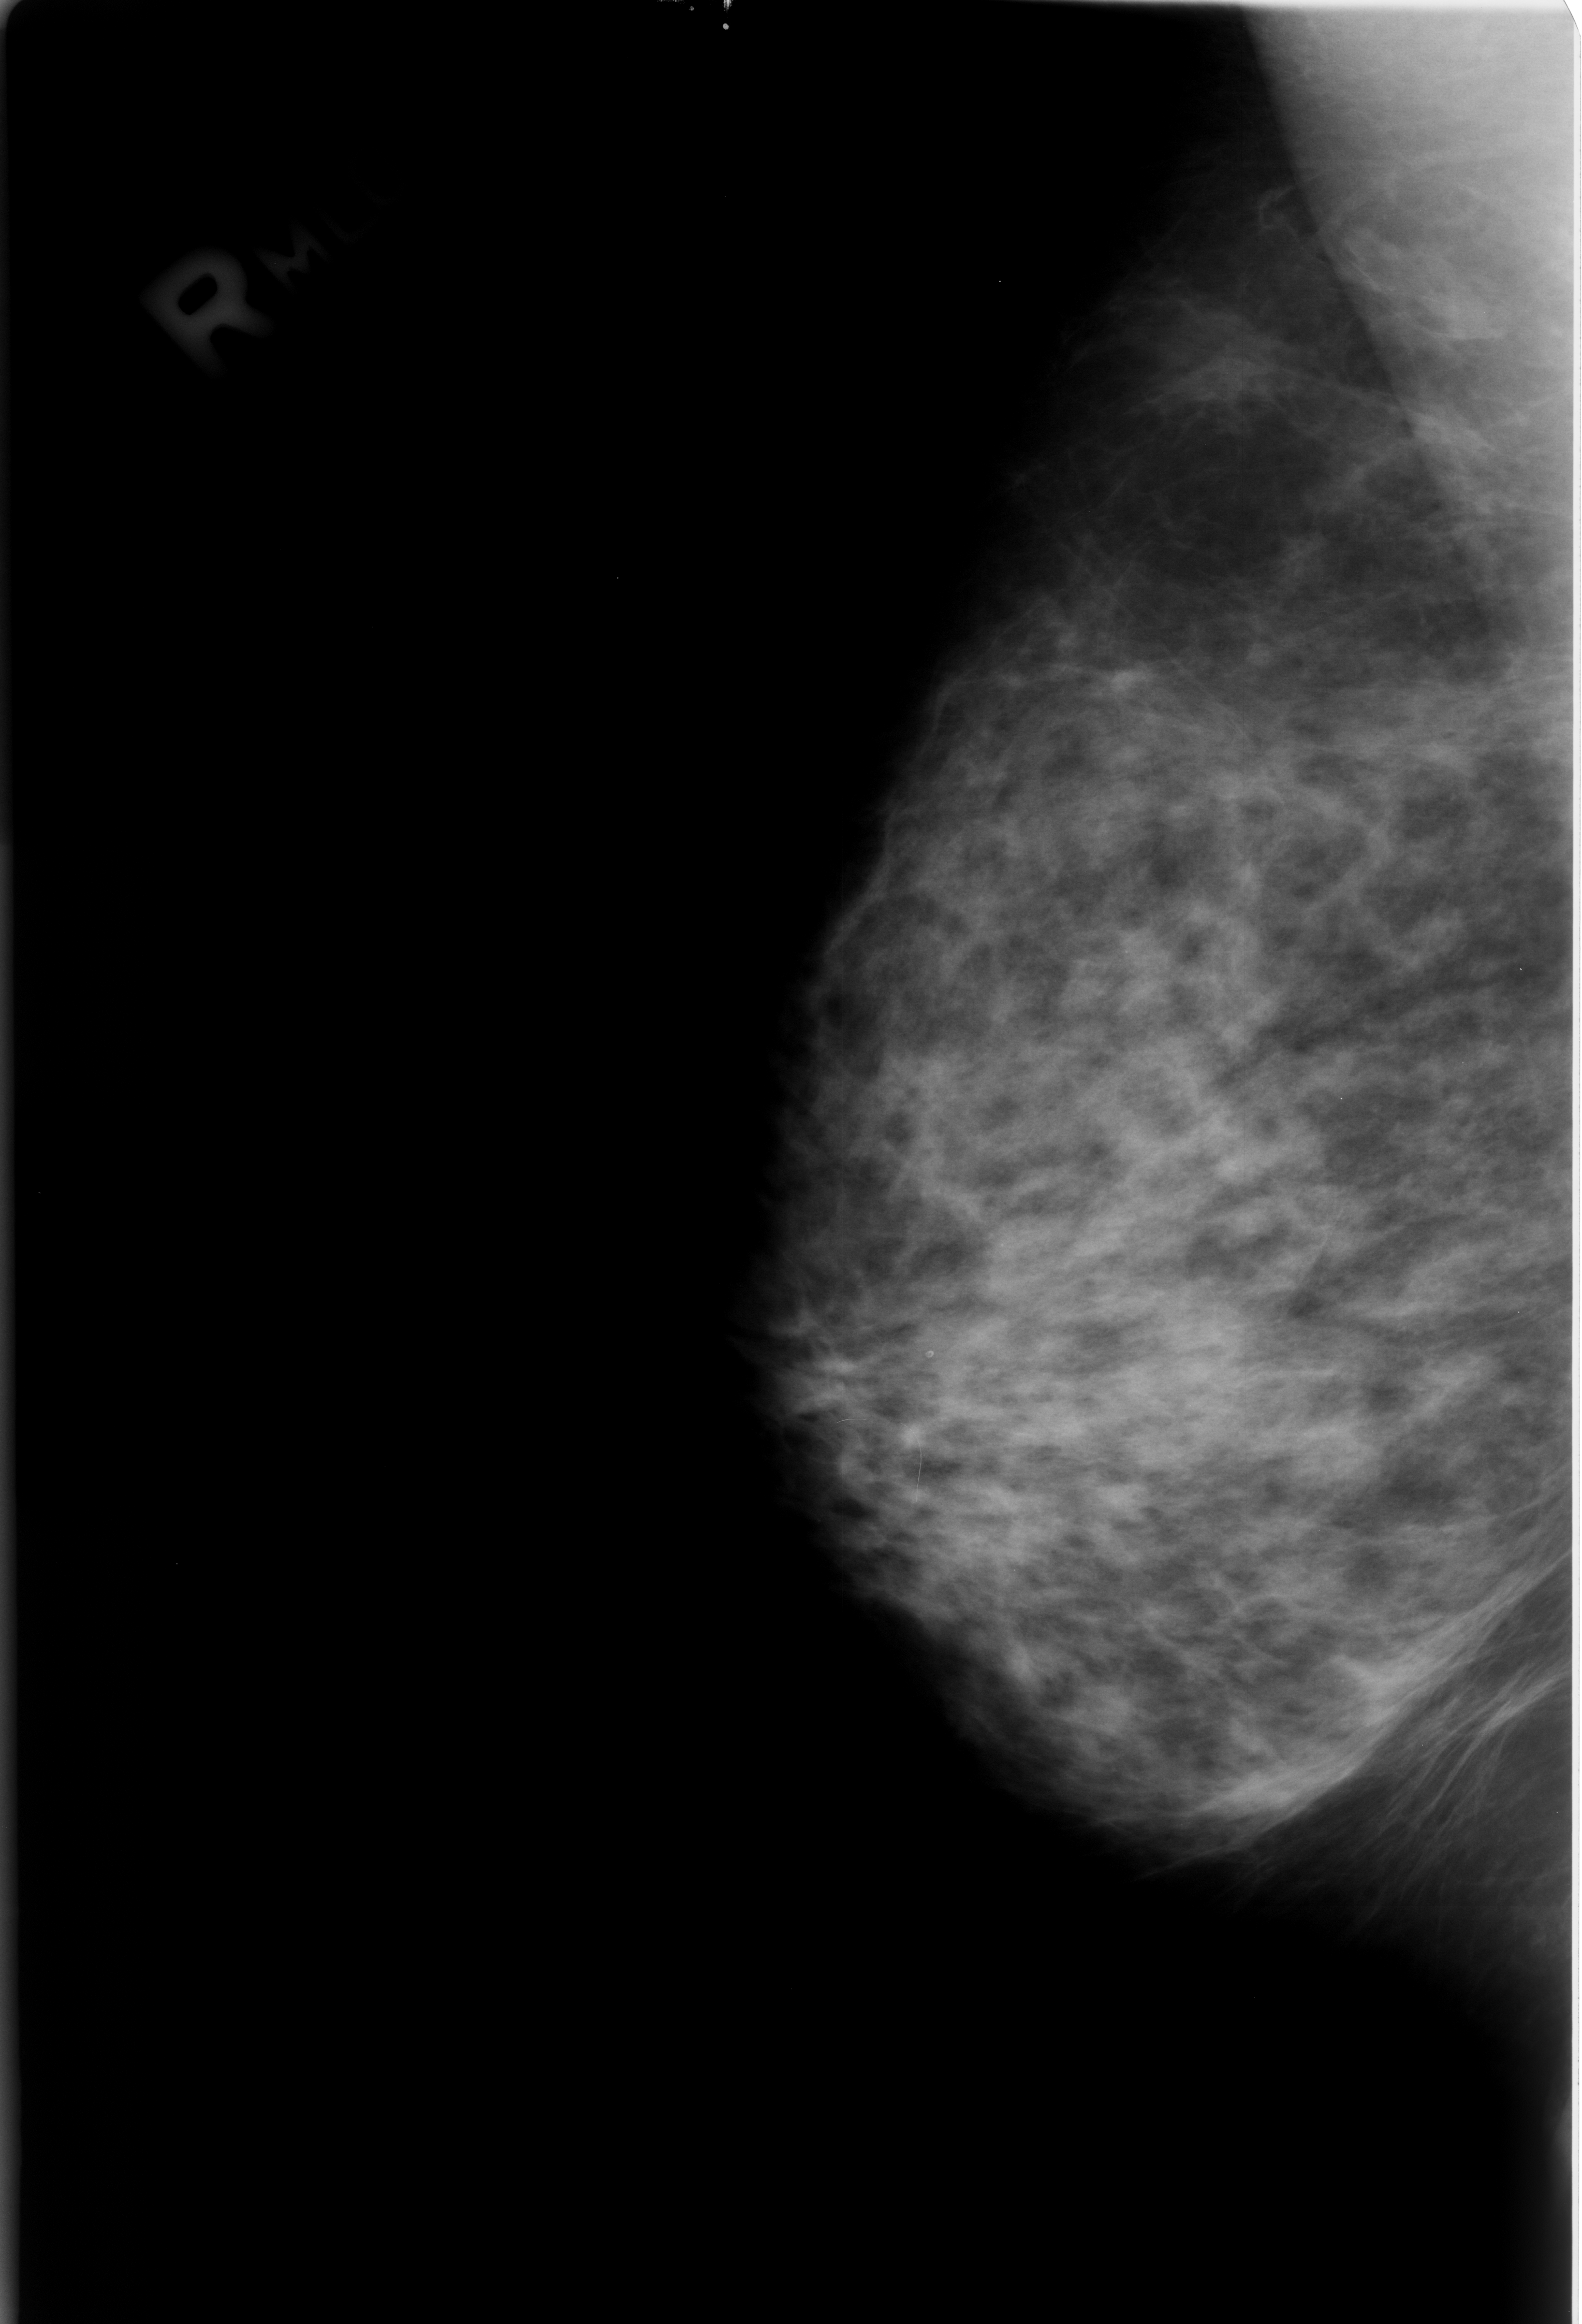
Digitized screen-film mammogram, right breast, mediolateral oblique (MLO) view.
Abnormality record for this image: calcifications, morphology lucent center; BI-RADS assessment category 2; subtlety rating 3 on a 1 (subtle) to 5 (obvious) scale; benign without callback (not worked up further).